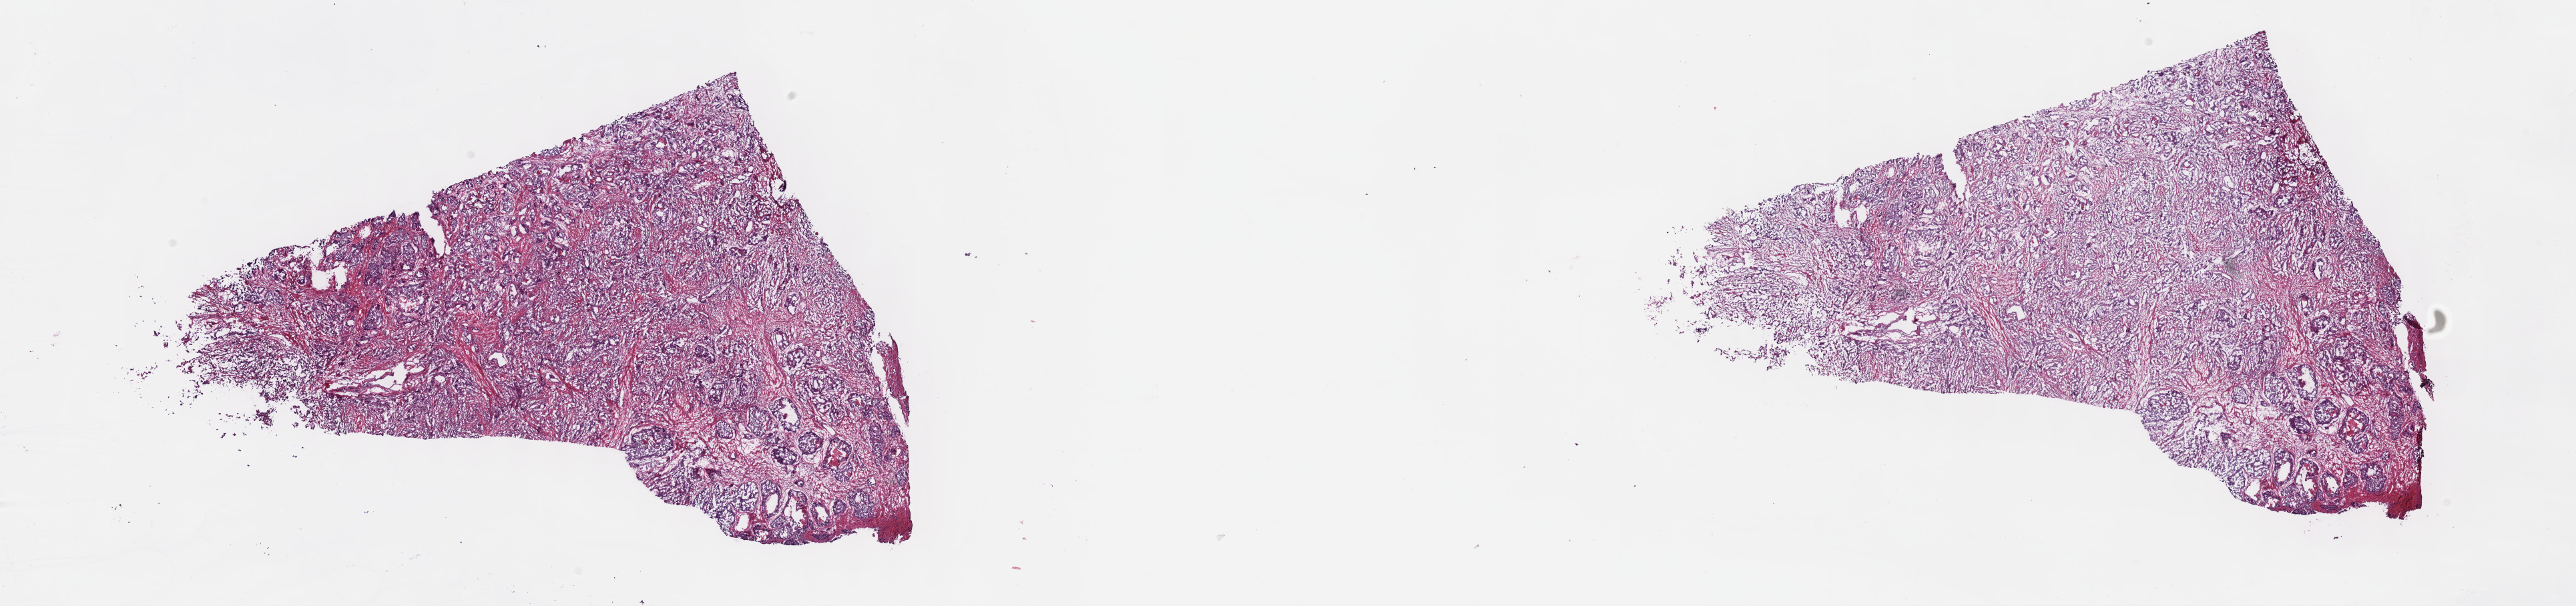
Whole-slide histology image, Hematoxylin and eosin (H&E) stained, low-resolution overview of the scanned area, about 31.2 x 7.3 mm; frozen section from the top of the tissue portion; sample: primary tumour, prostate. Patient: male, age at initial diagnosis 72 years. Gleason score: 9 (4+5). Pathologist review of this section (percent, as recorded): tumour cells 80%, tumour nuclei 90%, normal cells 0%, stromal cells 18%, necrosis 2%. Inflammatory infiltration, as recorded: lymphocyte infiltration 0%, monocyte infiltration 0%, neutrophil infiltration 0%.
* diagnosis: Adenocarcinoma, NOS
* lymph nodes positive (case pathology): 1 of 13 examined